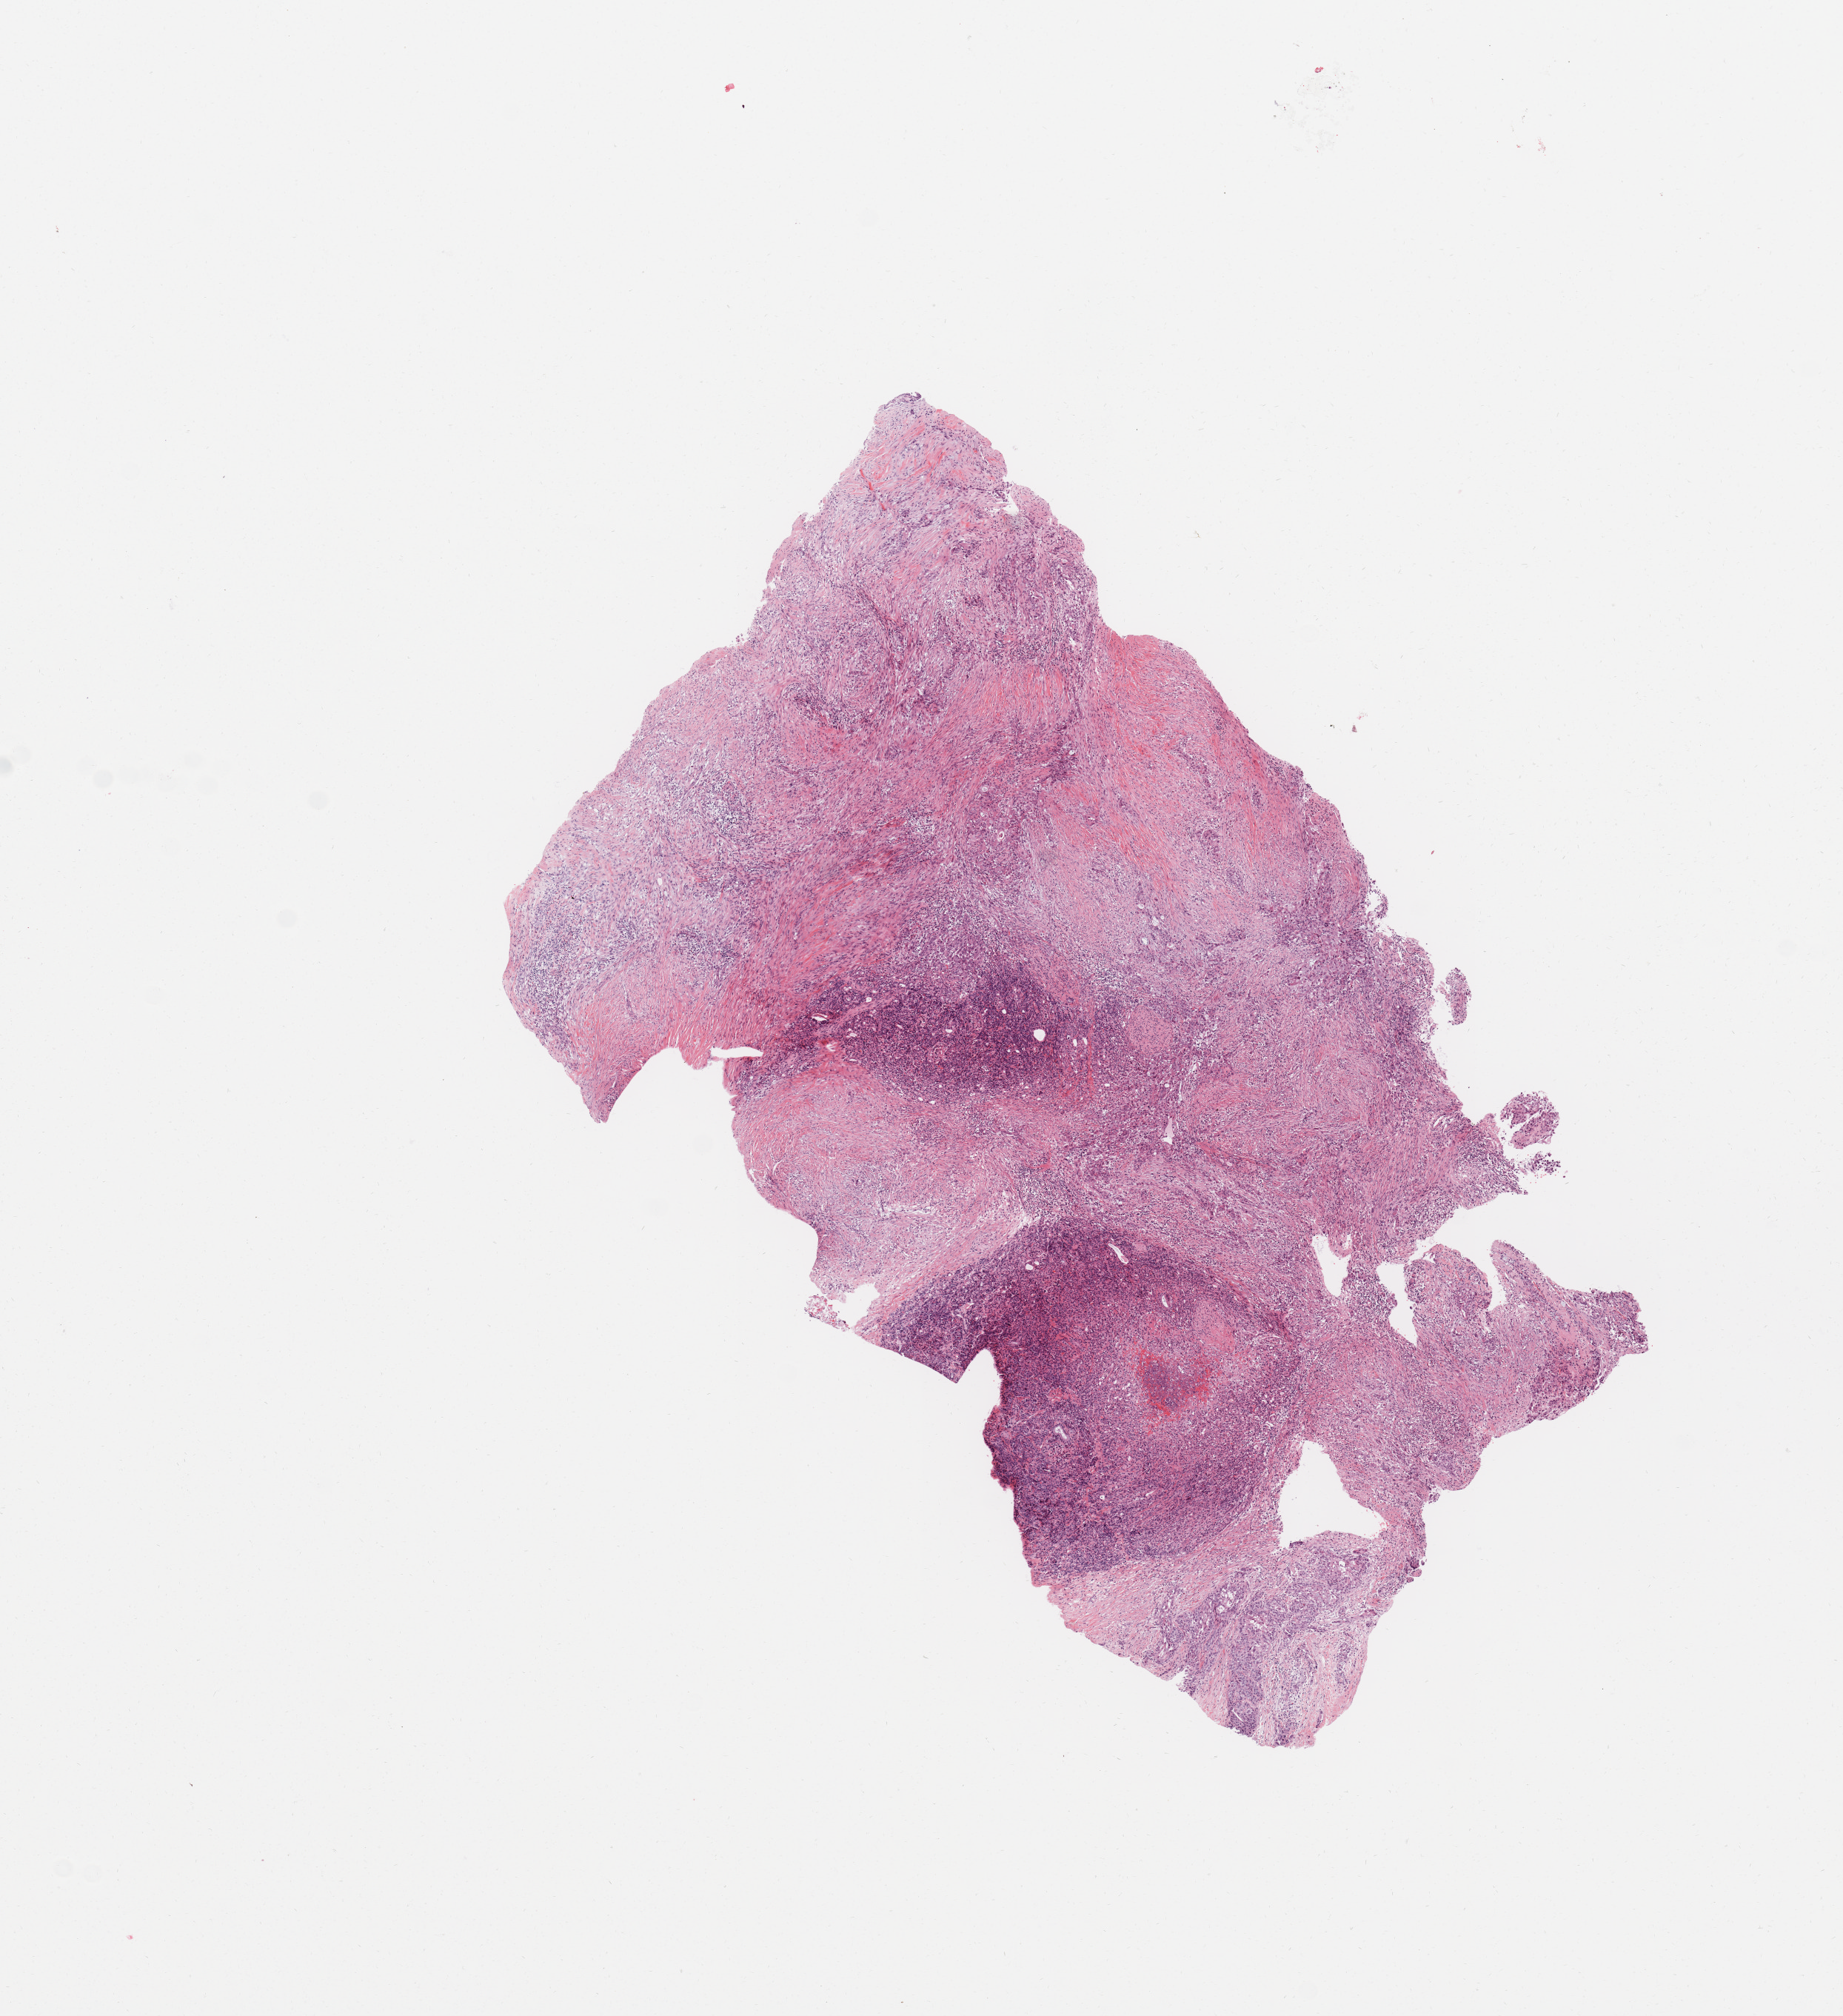
Whole-slide histology image, Hematoxylin and eosin (H&E) stained, shown as a low-resolution overview of the whole scanned area (about 9.8 x 10.8 mm, from a 20x scan); pancreas, tumour tissue. Patient: male, age 73 years.
Primary tumour site (as recorded): head. Patient diagnosis (cohort enrolment): ductal adenocarcinoma (pancreas).